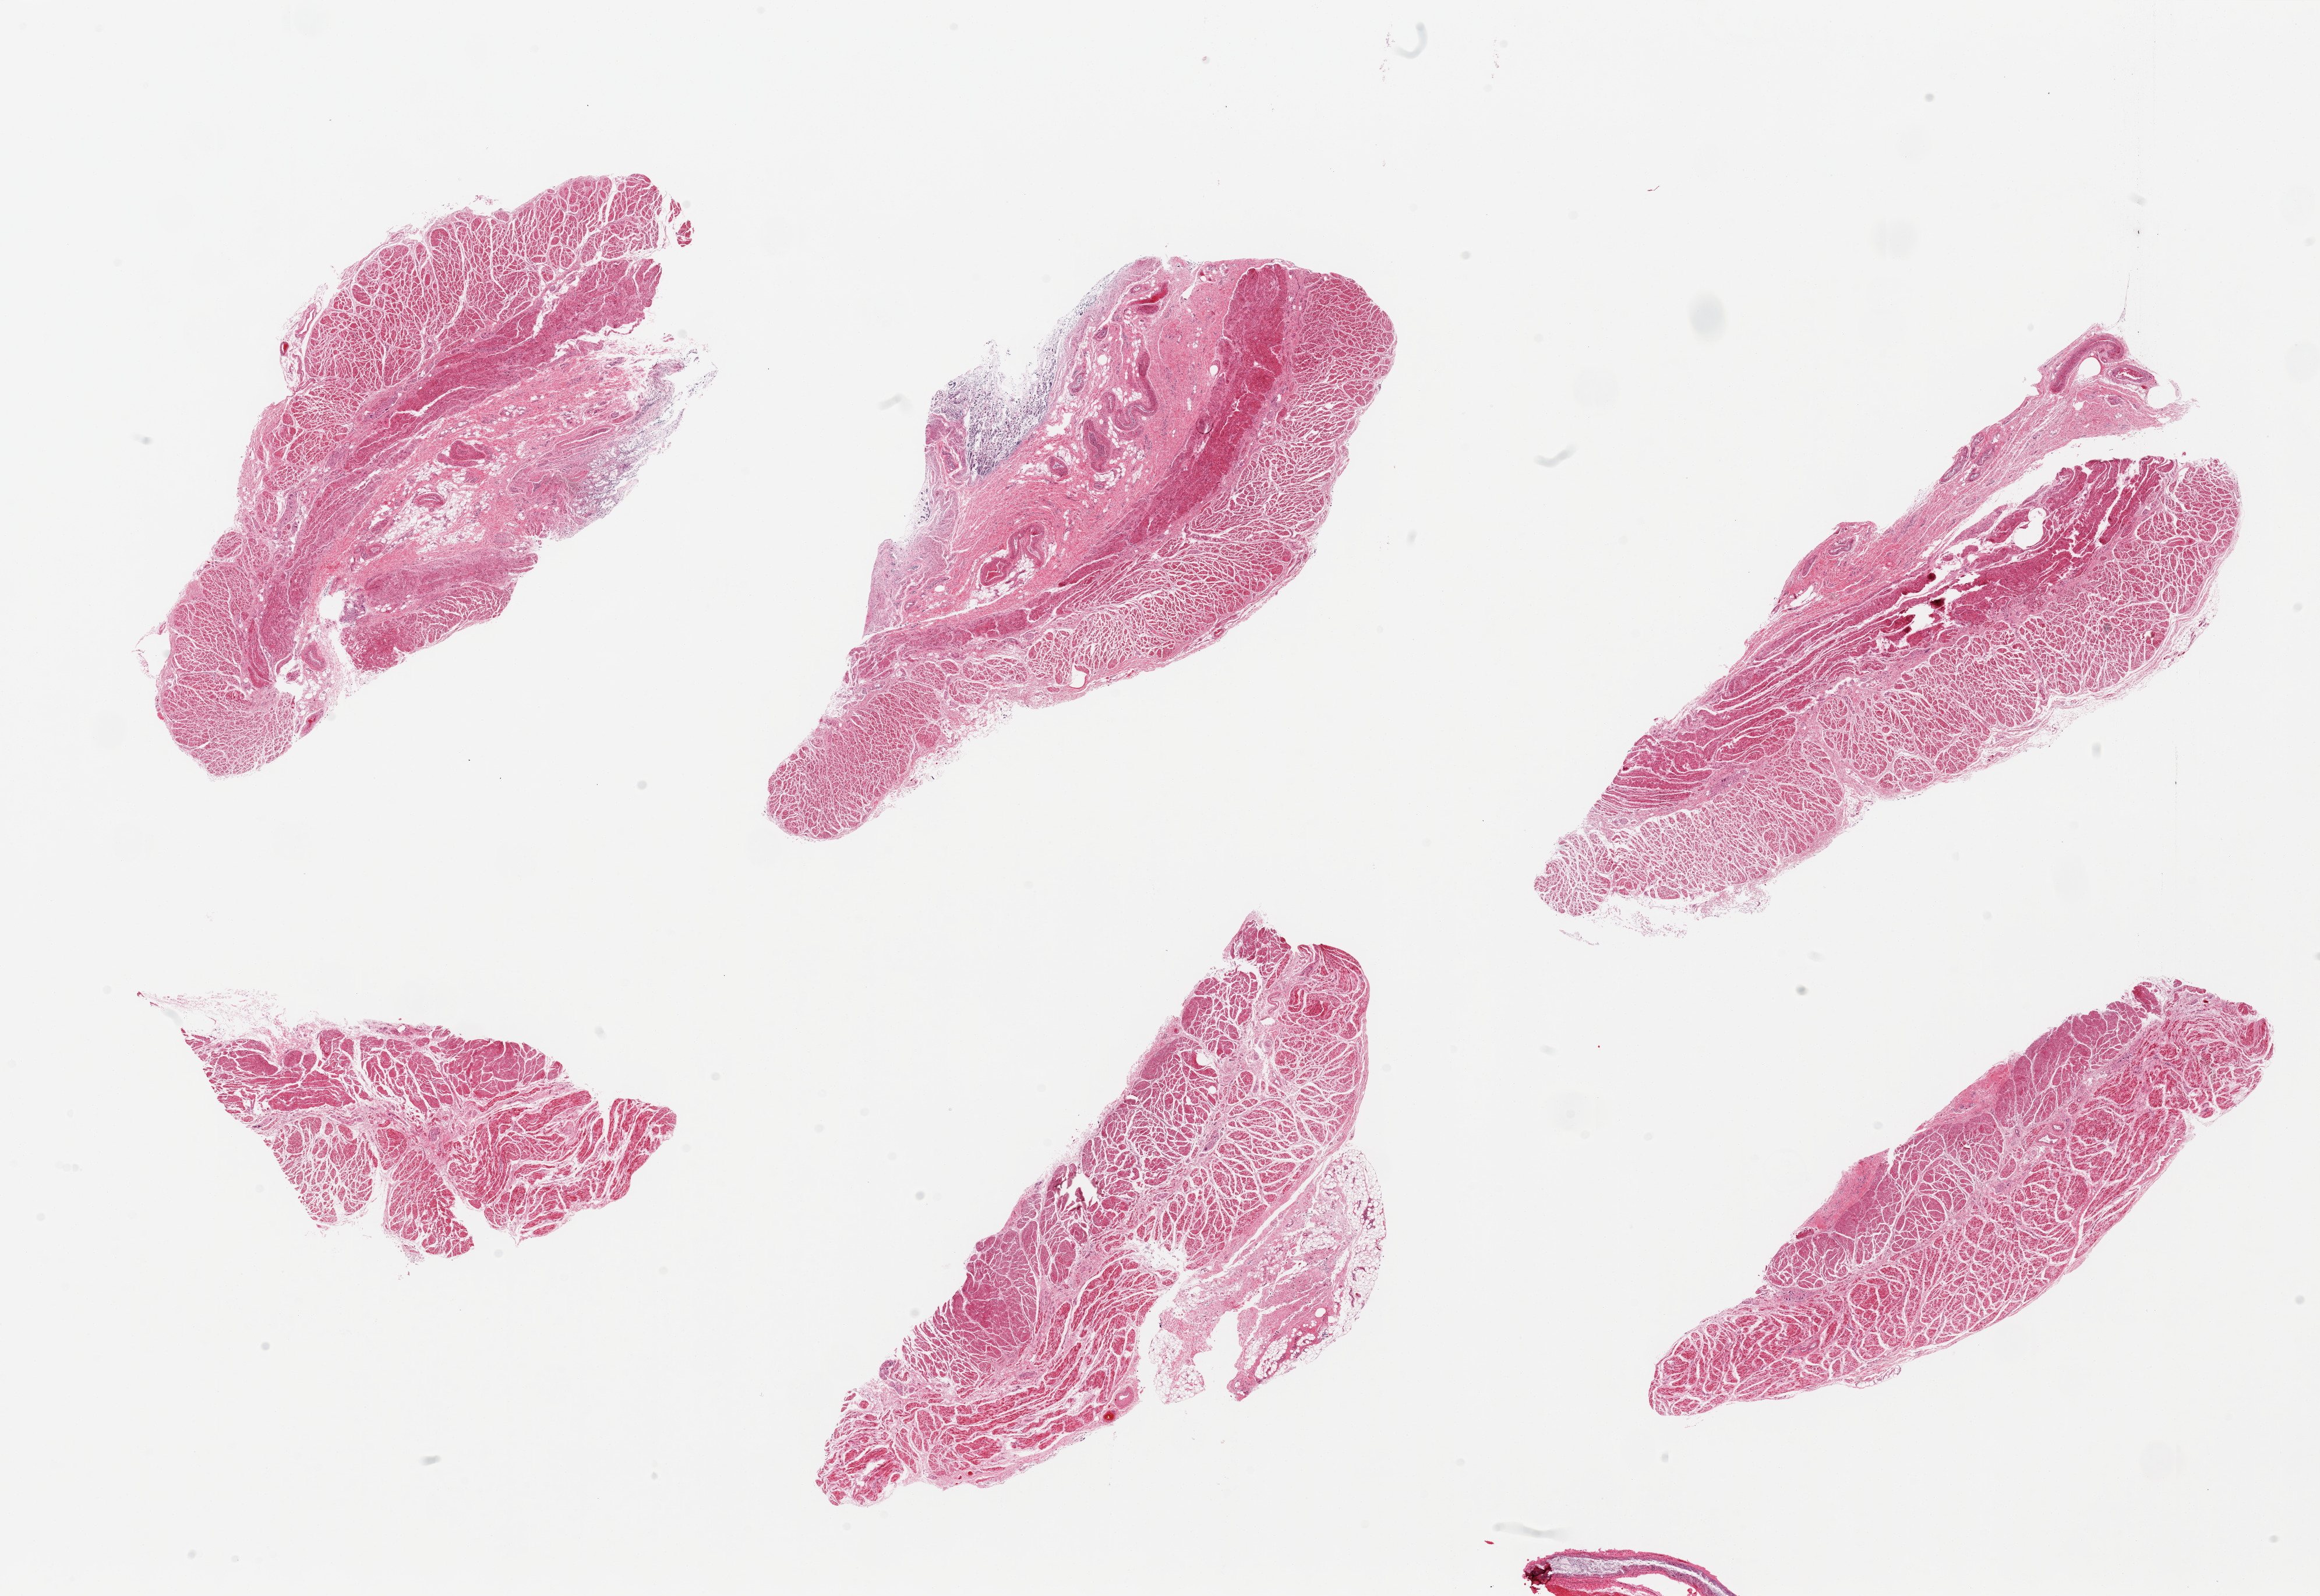
Digitized H&E-stained section, brightfield — whole scanned area (about 31.5 x 21.7 mm, slide scanned at 20x) shown as a low-resolution overview. PAXgene-fixed paraffin-embedded (PFPE) section. Sampled site (target tissue): gastroesophageal junction. Tissue donor sample. Donor sex: male.
Reviewer comment on this tissue sample: 6 pieces, all muscularis, trace adherent autolyzed mucosa.